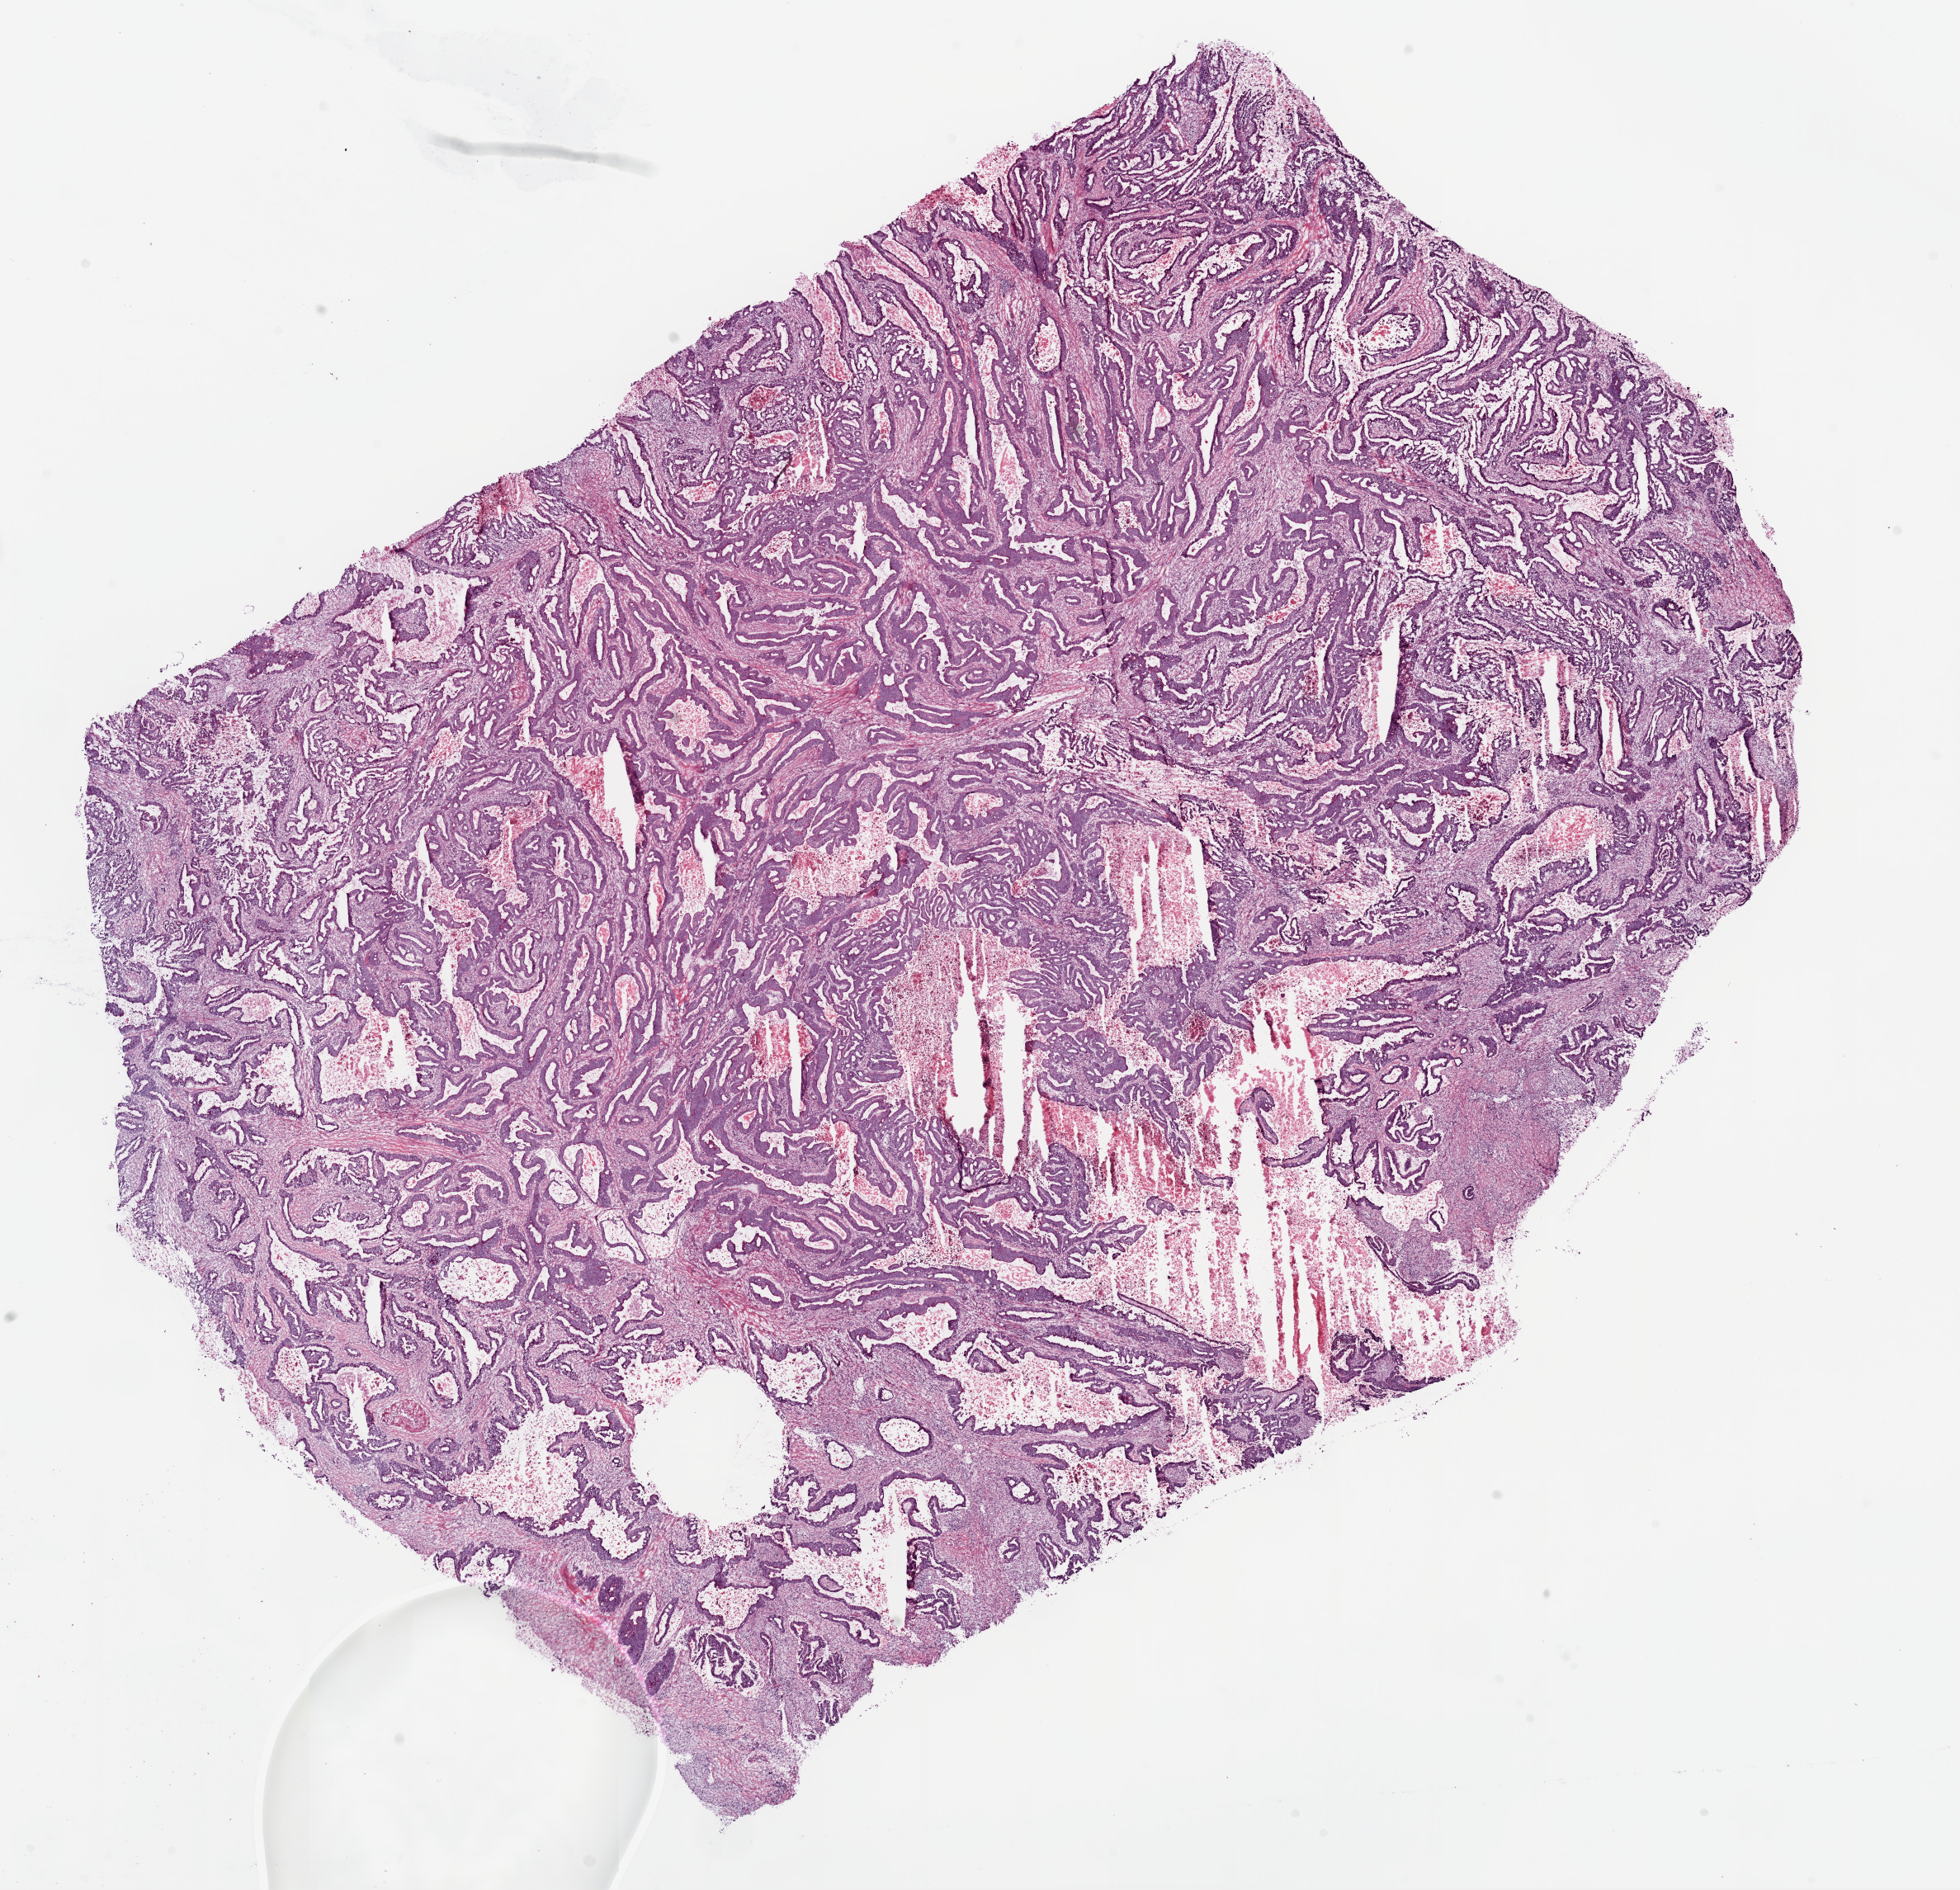
Digitized H&E-stained tissue section (whole slide), low-resolution overview of the scanned area, about 19.1 x 18.4 mm (slide scanned at 20x); frozen section from the bottom of the tissue portion; primary tumour sample from the colon. Patient: female, age at initial diagnosis 42 years. Slide review estimates, as recorded: tumour cells 65%, tumour nuclei 75%, normal cells 0%, stromal cells 15%, necrosis 20%.
AJCC pathologic stage: IIA (6th edition). Pathologic diagnosis: Adenocarcinoma, NOS.